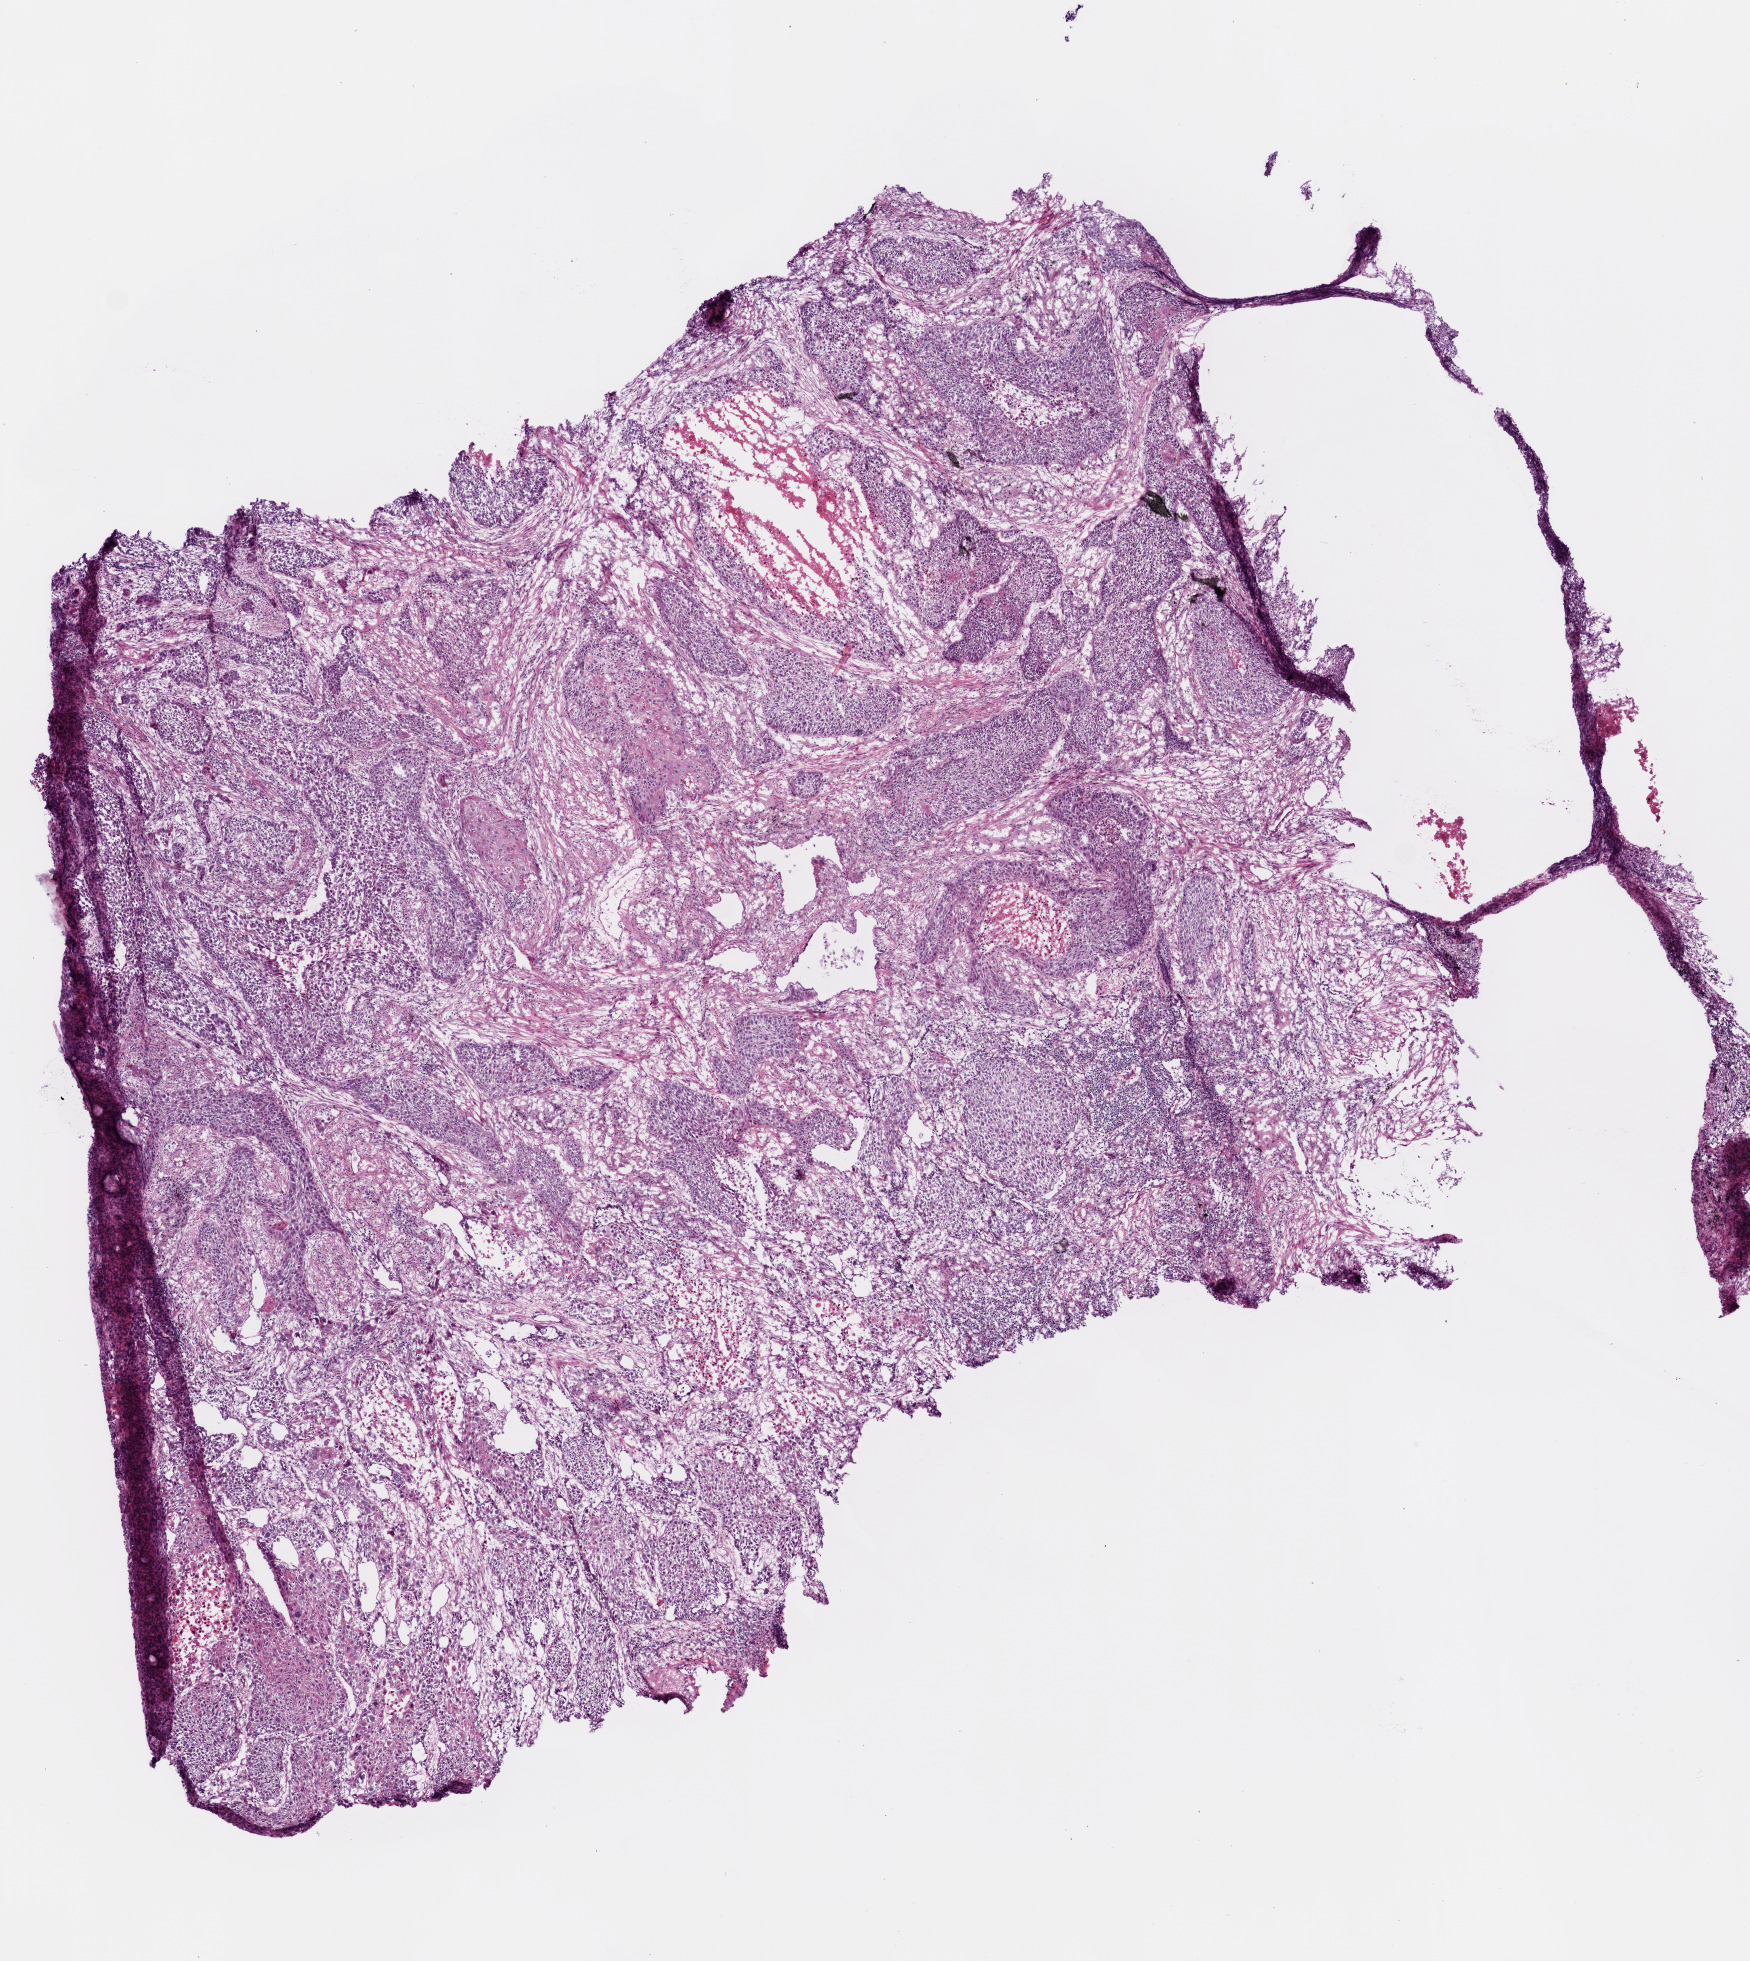
Hematoxylin and eosin (H&E) stained whole-slide image, a low-resolution overview of the entire scanned area, about 7.0 x 7.9 mm (slide scanned at 20x), frozen section from the top of the tissue portion, sample: primary tumour, lung. Patient: male, age at initial diagnosis 72 years. Pathologist review of this section (percent, as recorded): tumour cells 40%, tumour nuclei 80%, normal cells 0%, stromal cells 58%, necrosis 2%. Infiltration values recorded for this section: lymphocyte infiltration 10%.
- AJCC pathologic stage: IIB (5th edition)
- pathologic diagnosis: Squamous cell carcinoma, NOS (middle lobe, lung)
- laterality: right